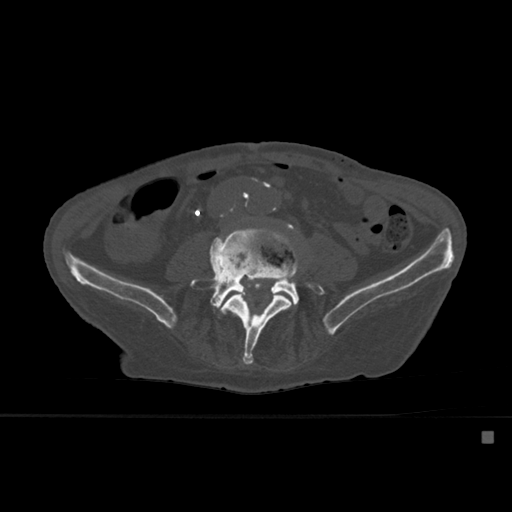
CT including the spine, one axial slice. Position 186 of 527 along the scan axis. Bone window (W 1800 / L 400 HU). 1.5 mm slice thickness. 512 × 512 image matrix, field of view 373 × 373 mm. Male patient, age 78 years. From the clinical record (not read from this slice): primary cancer: prostate.
Annotated regions visible in this slice (semi-automatically segmented with operator editing):
- L4 vertebra: bounding box [x1, y1, x2, y2] px = [221, 253, 300, 364]
- L5 vertebra: [190, 227, 325, 315]